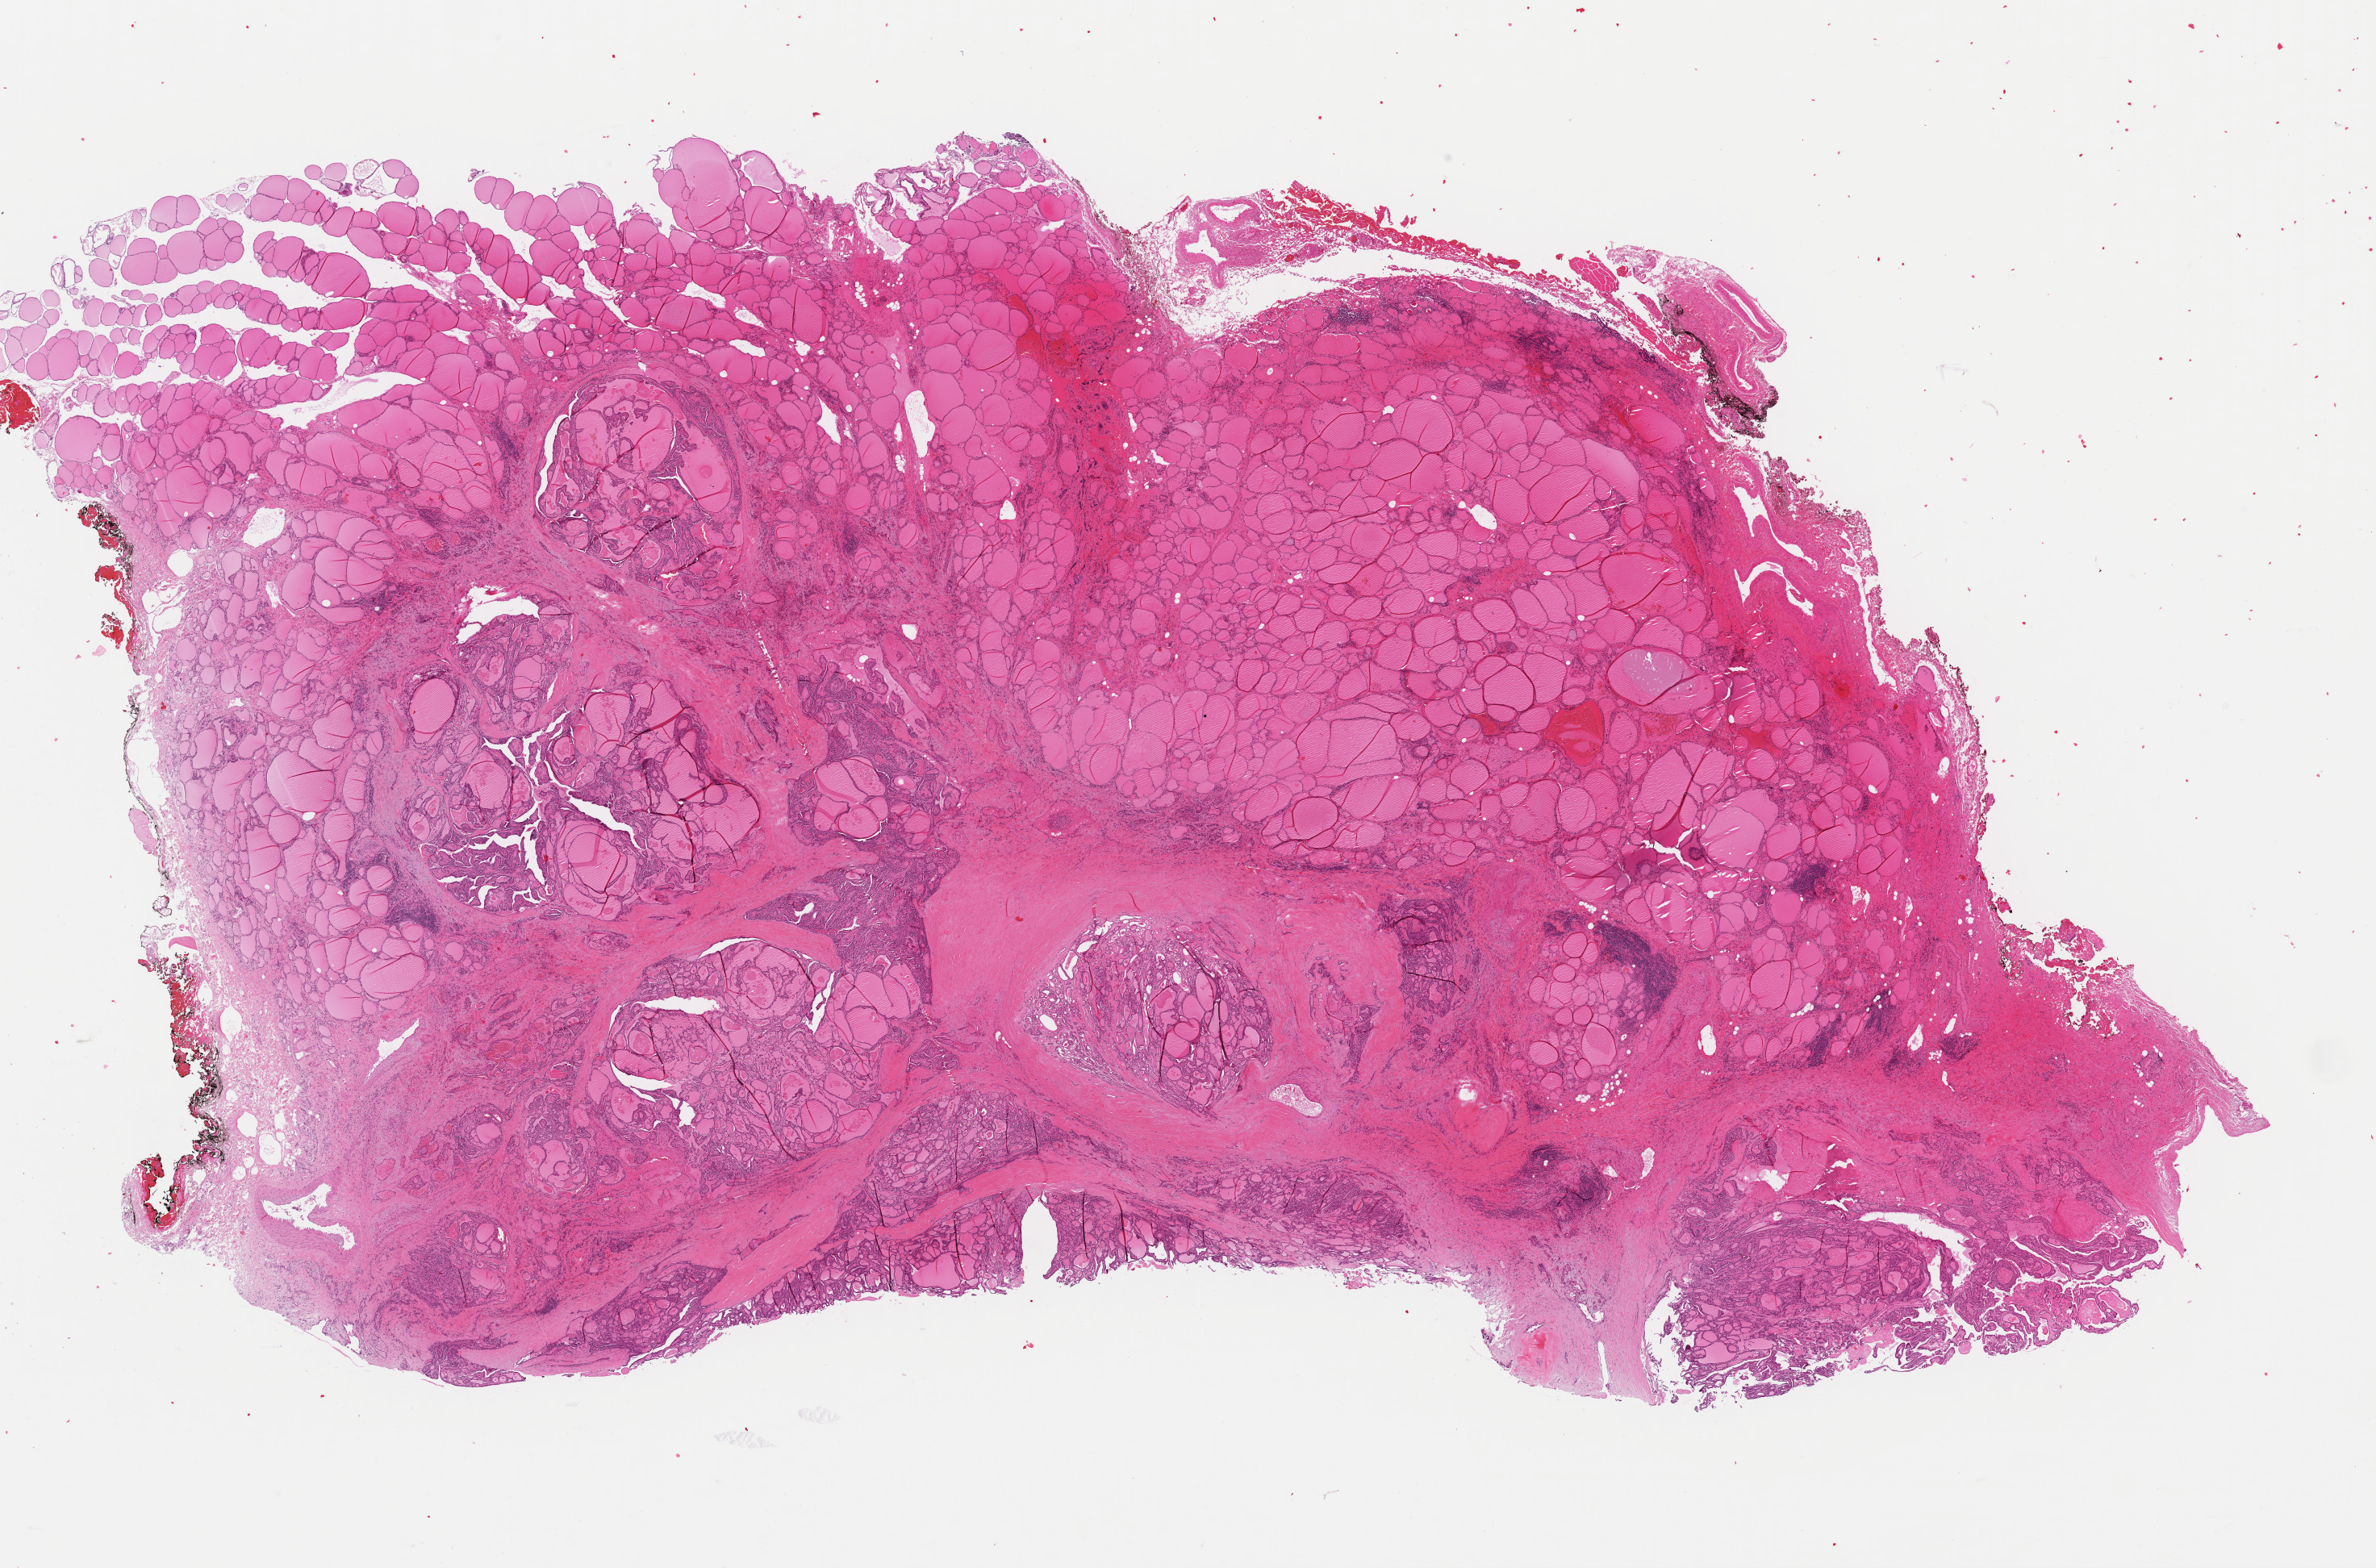
Whole-slide histology image, H&E — shown as a low-resolution overview of the whole scanned area (about 23.3 x 15.4 mm, from a 40x scan); formalin-fixed paraffin-embedded (FFPE) diagnostic section; thyroid, primary tumour sample. Patient: female, age at initial diagnosis 31 years.
Lymph nodes positive (case pathology): 1 of 4 examined. AJCC pathologic stage: I (7th edition). Diagnosis: Papillary adenocarcinoma, NOS (thyroid gland).